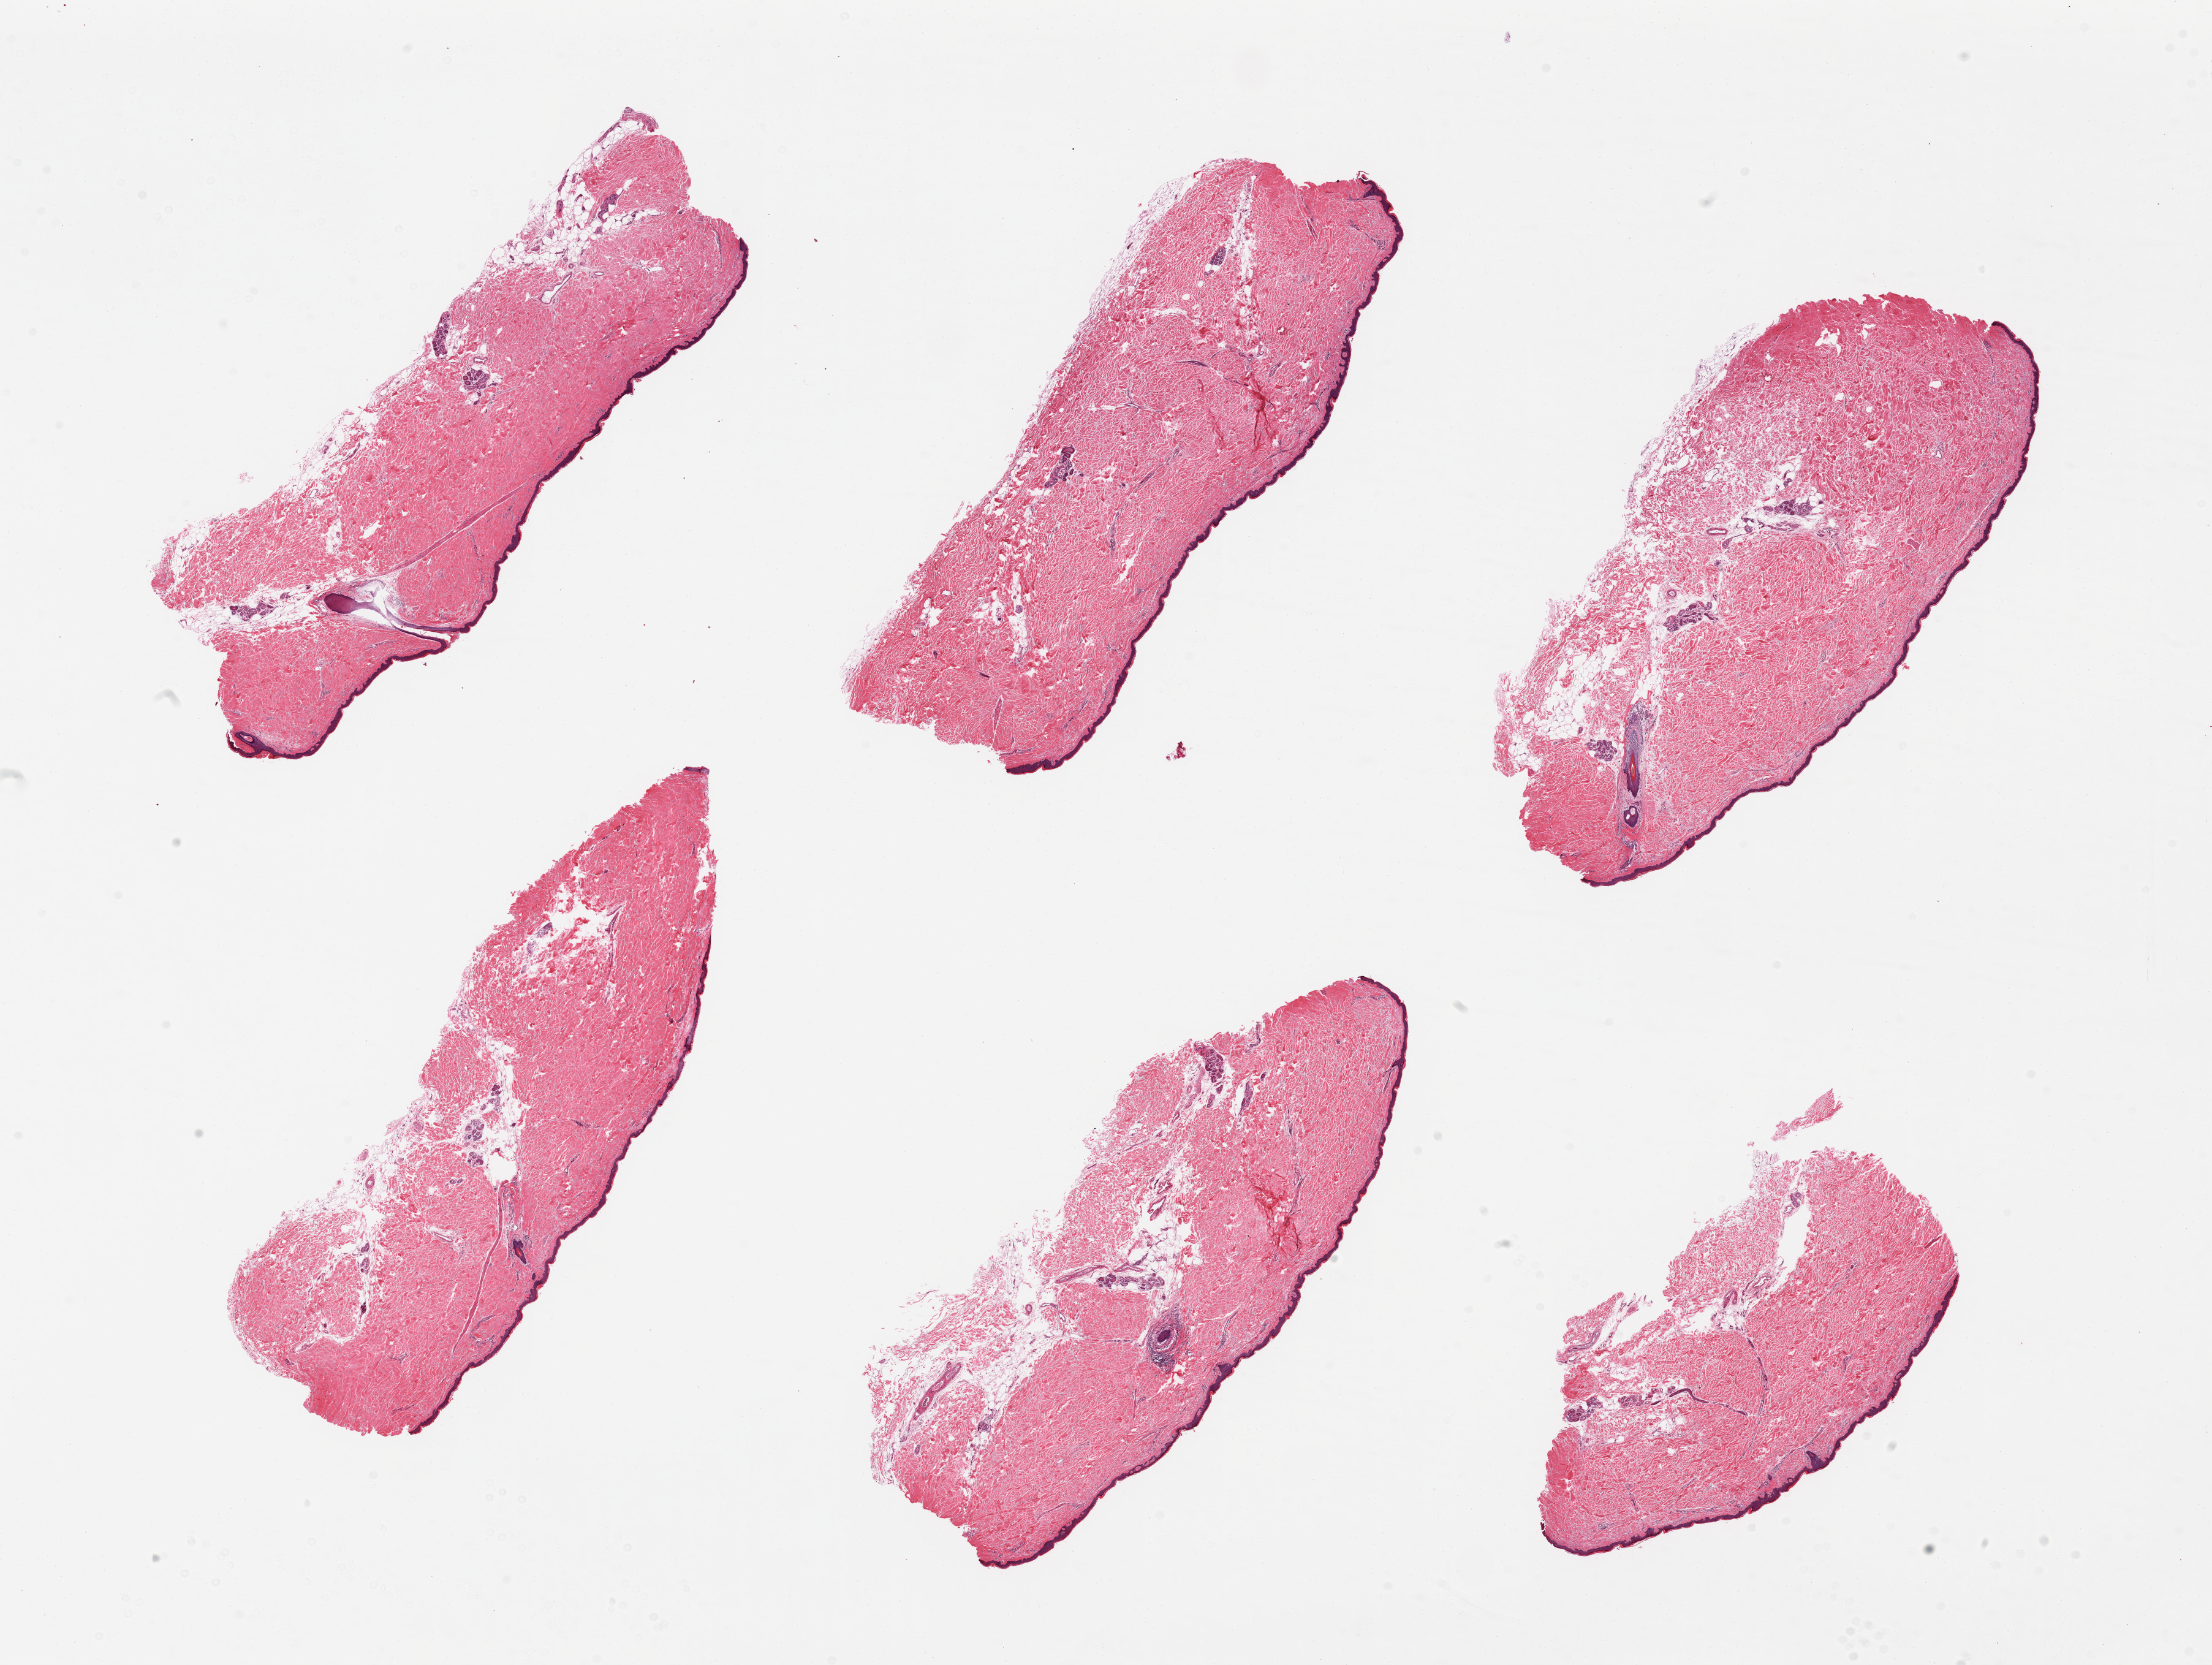
Digitized hematoxylin and eosin (H&E)-stained section, brightfield — low-resolution overview of the scanned area, about 28.5 x 21.5 mm; PAXgene-fixed paraffin-embedded (PFPE) section; target tissue: skin of lower leg; donor tissue sample. Donor: male.
* review note (as recorded): 6 pieces, relatively well trimmed and with minimal internal fat, squamous epithelium measures 38-43 microns